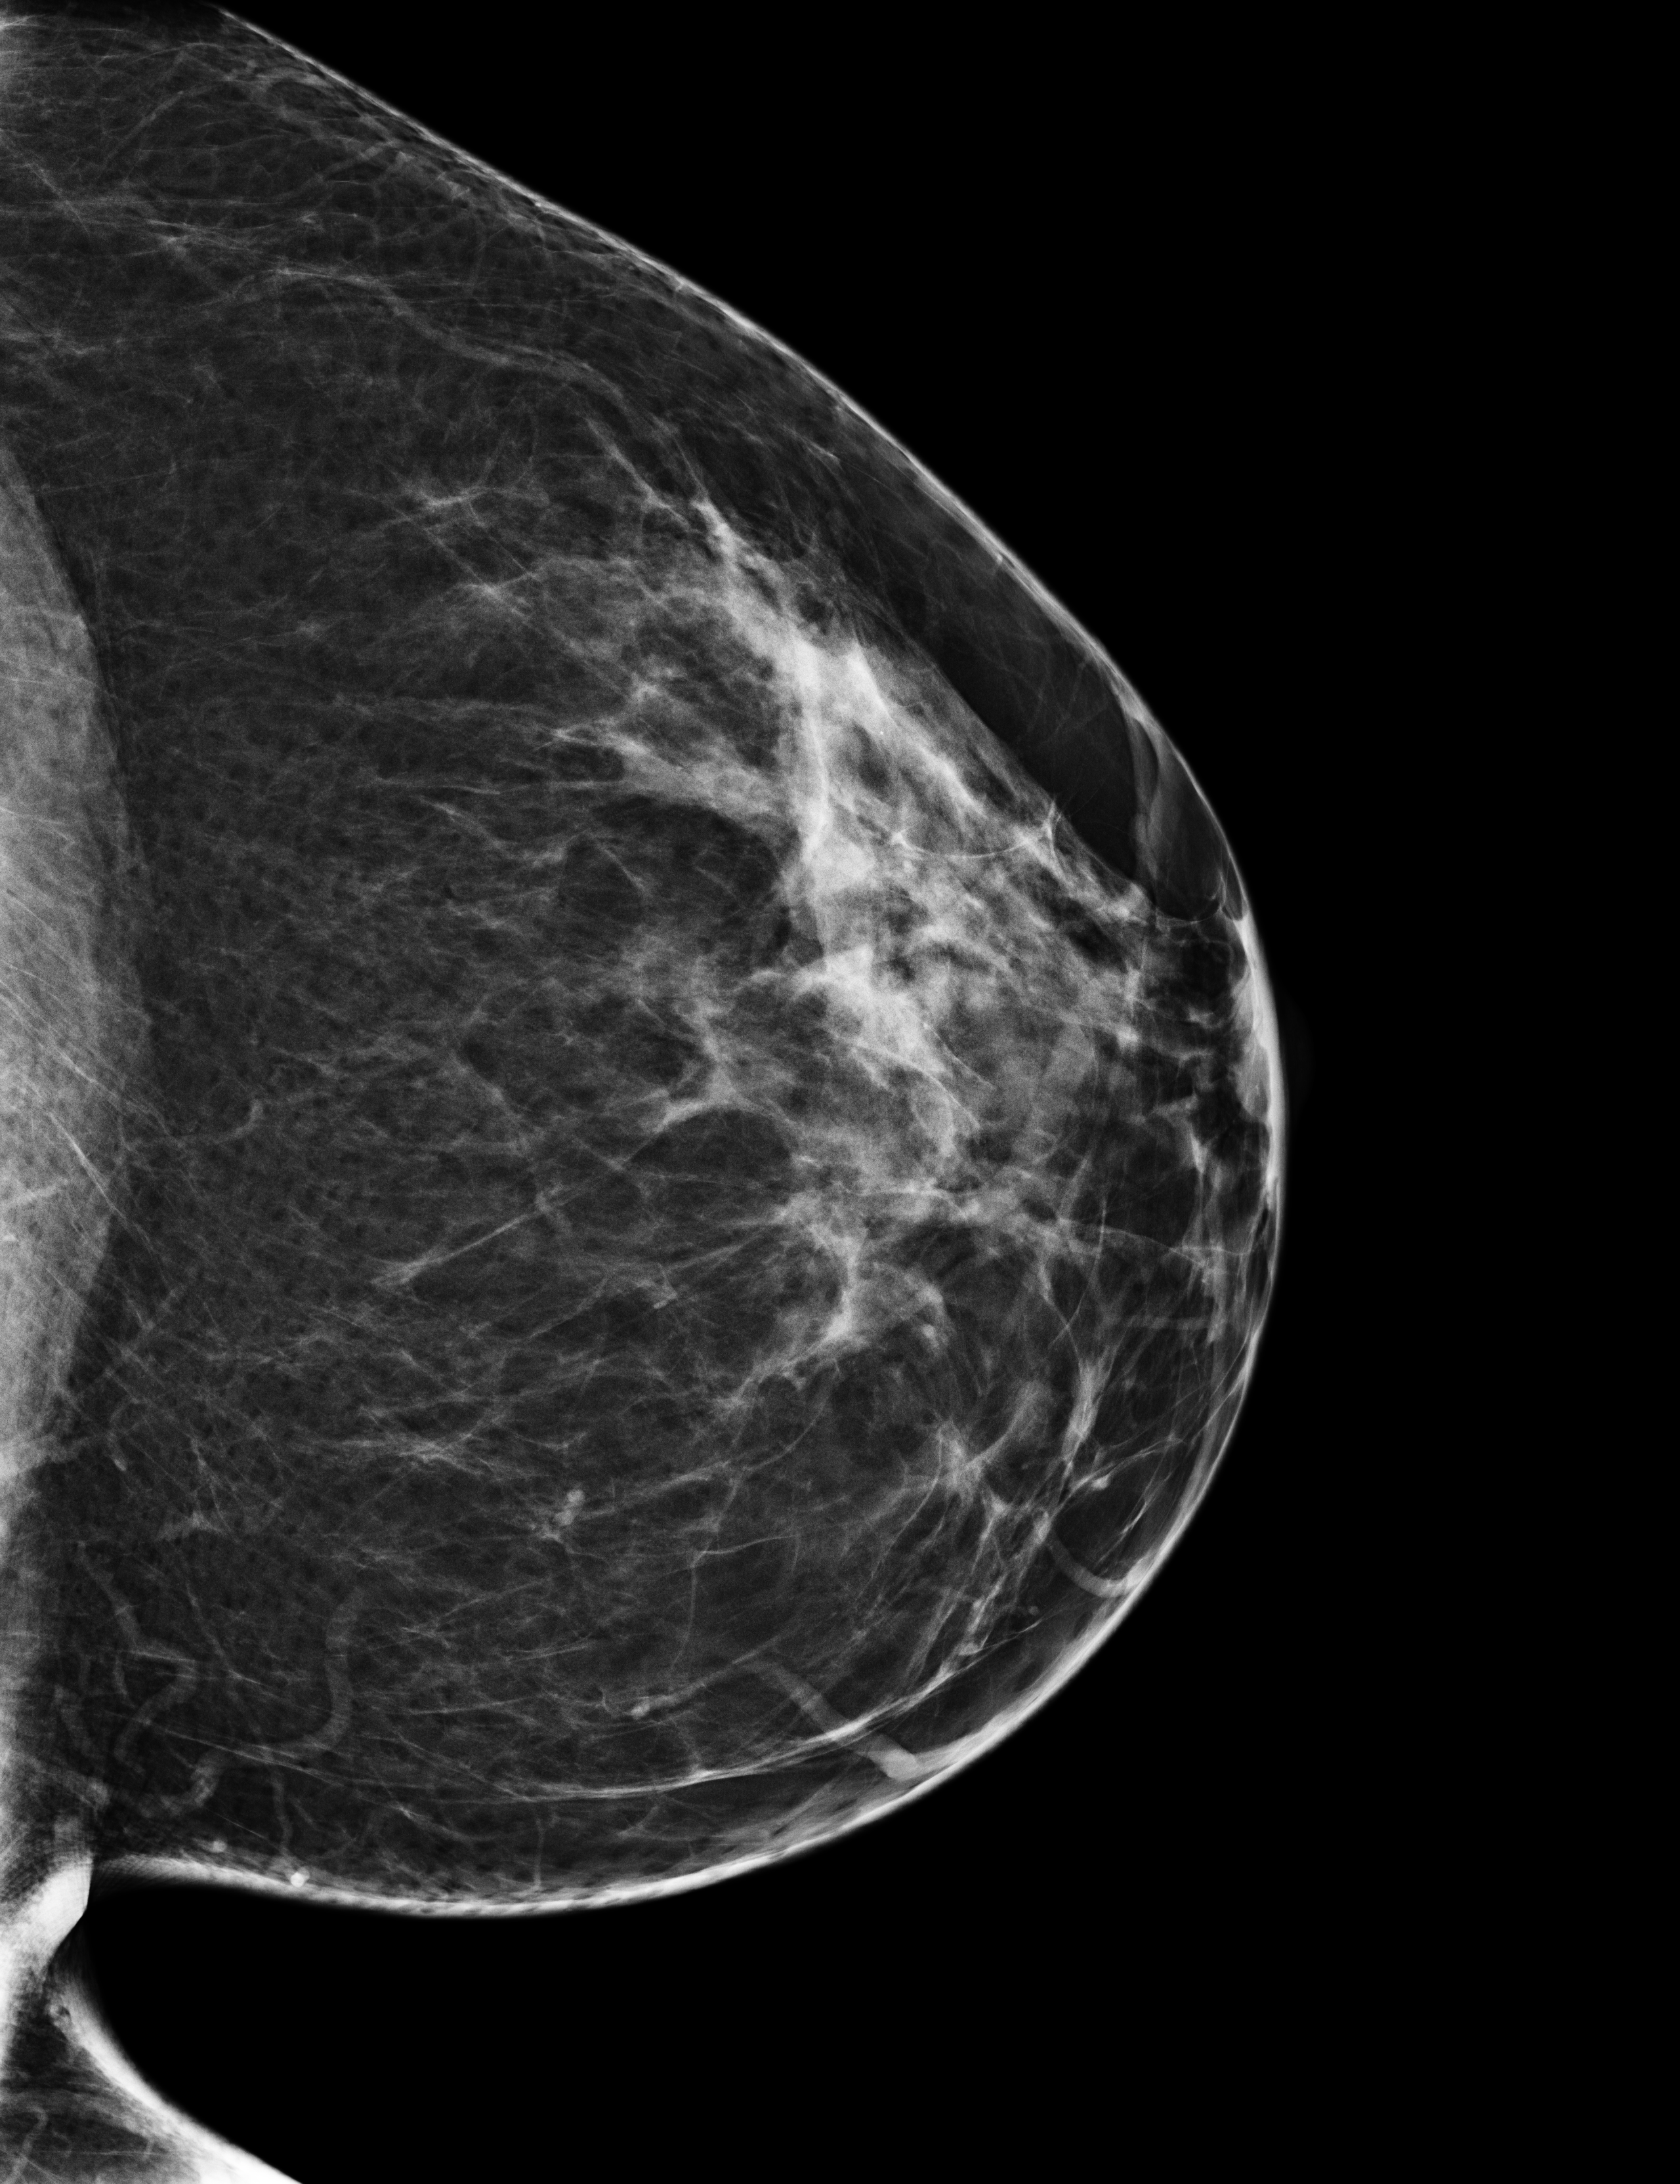
Annual screening mammography examination; system: Selenia Dimensions. Female patient, age 42 years.
Image type: full-field digital mammogram. Breast: left. Projection: craniocaudal (CC) view.